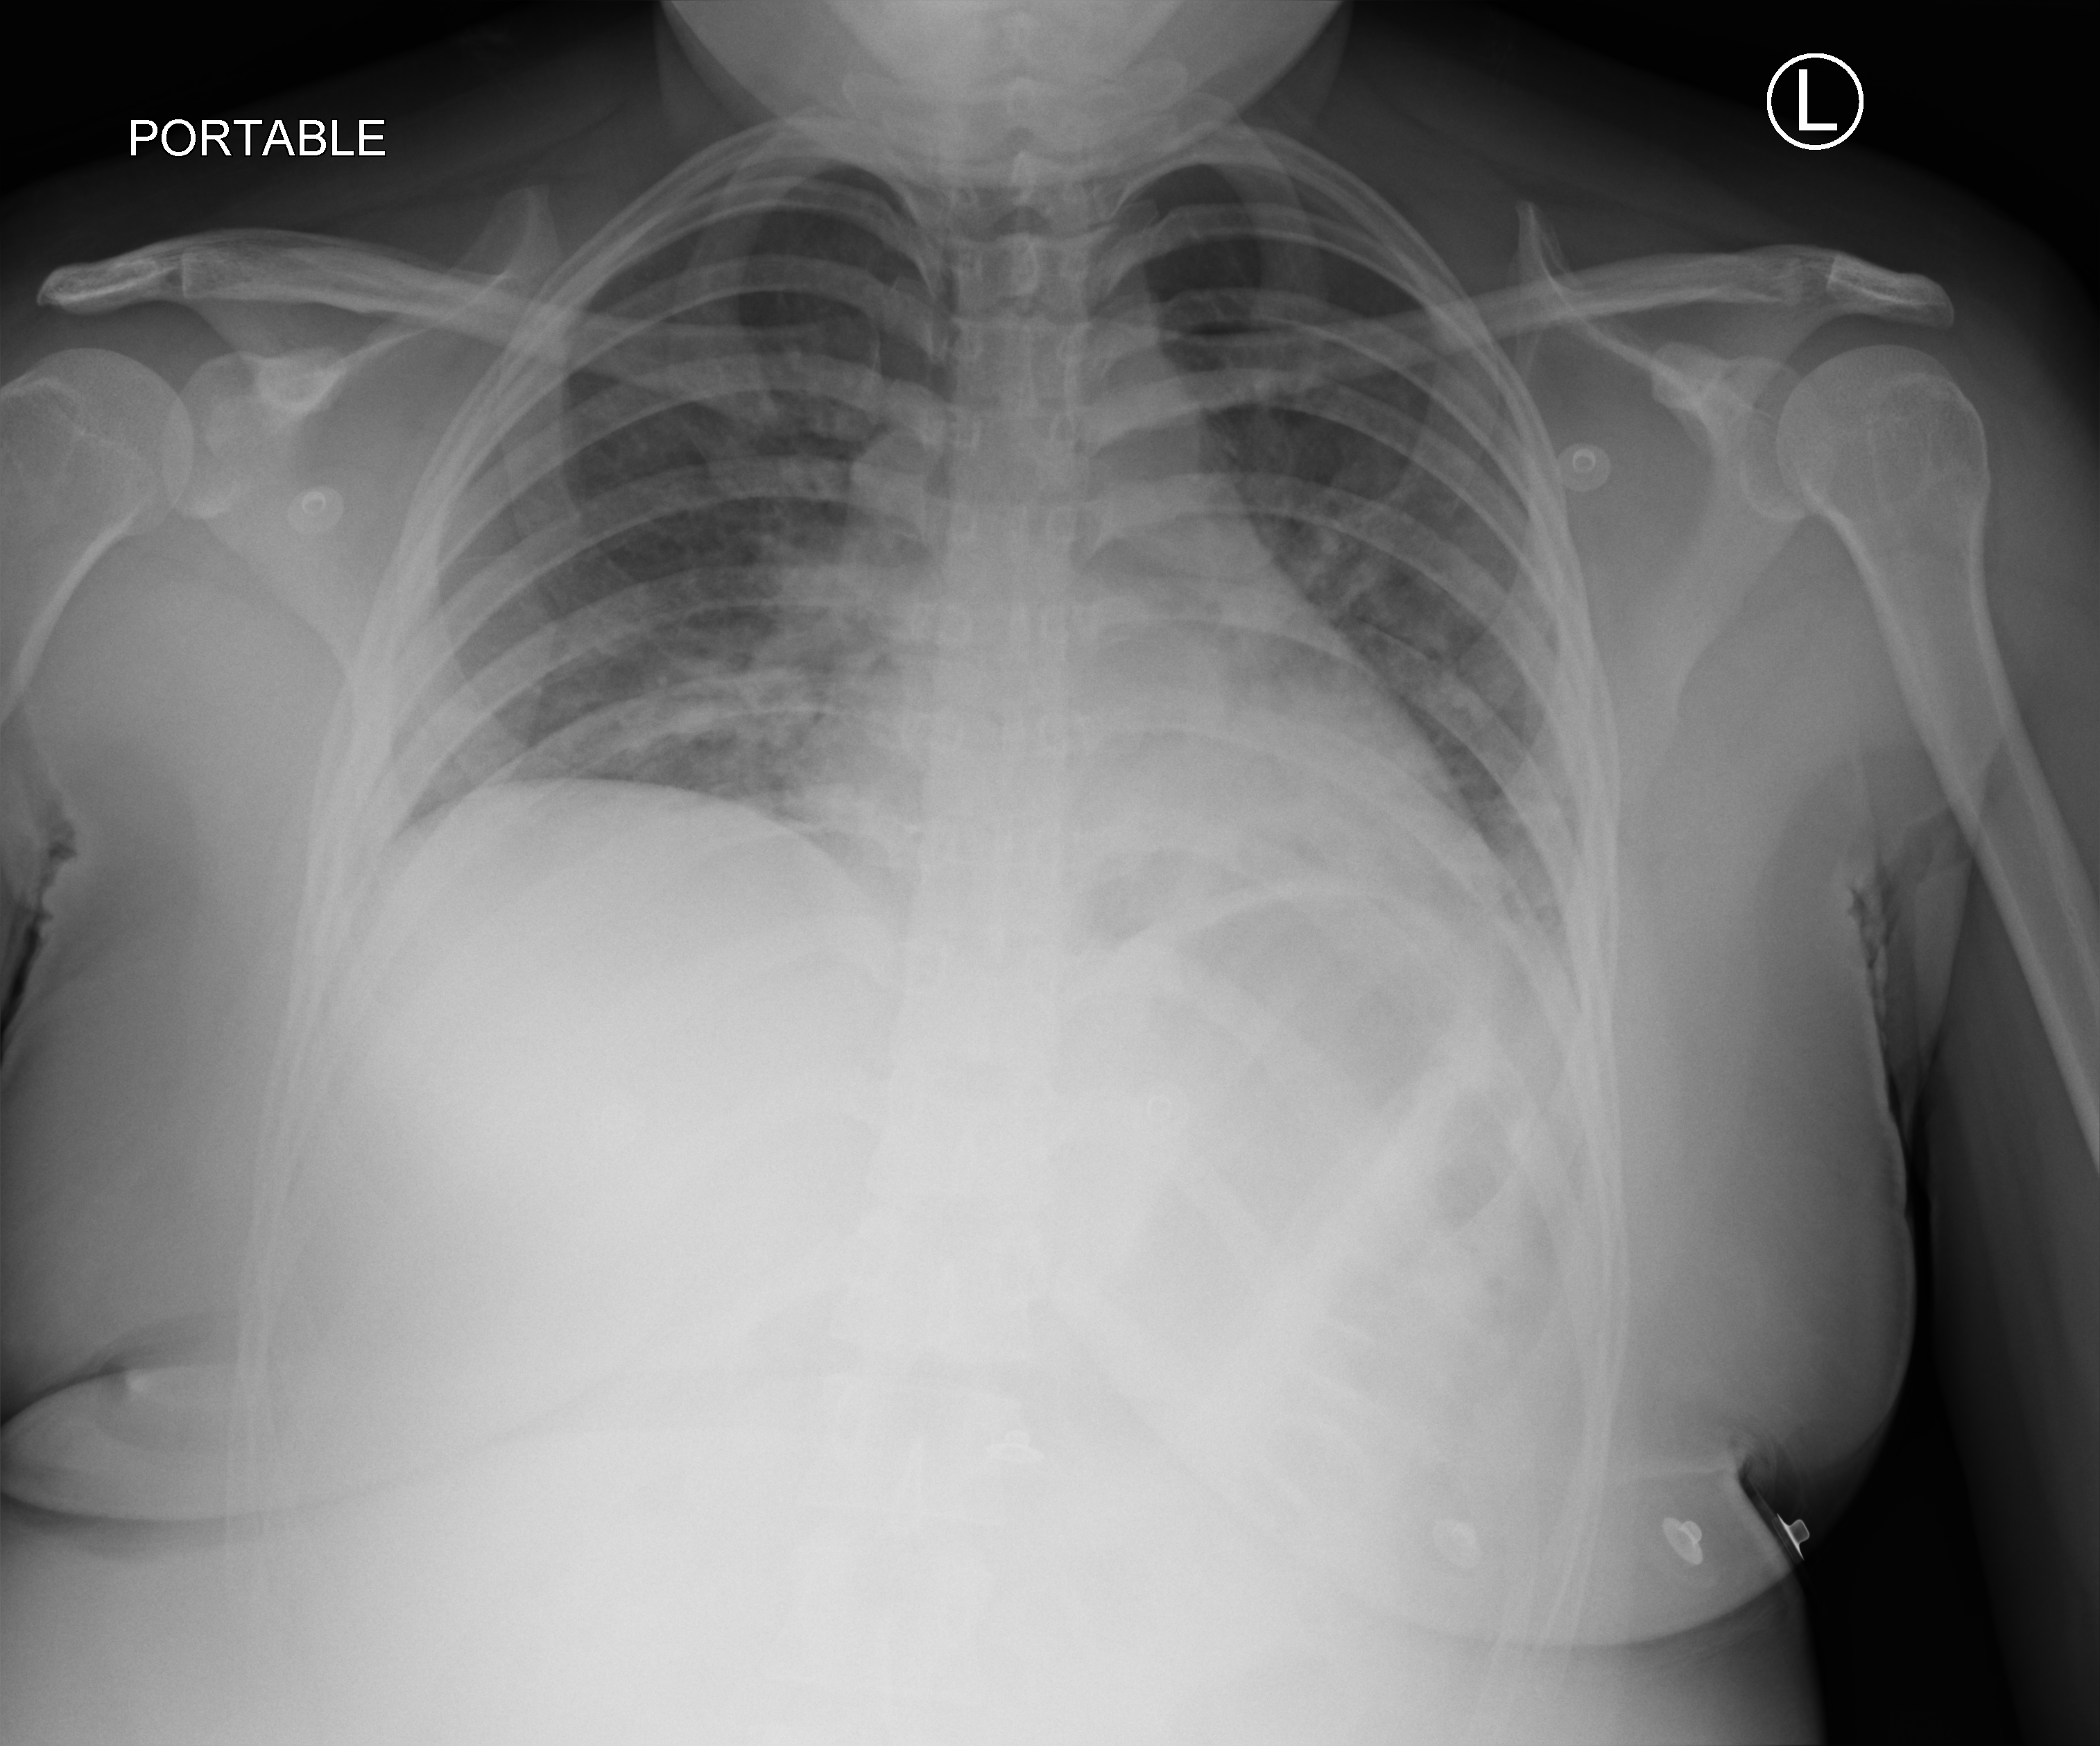
Chest X-ray (portable). Female patient hospitalised with COVID-19, age 18–59 years.
Admission-level facts for this patient (not findings on this image; timing relative to this image not recorded):
- length of hospital stay: 11 days
- admitted to intensive care during this hospital stay: no
- mechanically ventilated during this hospital stay: no